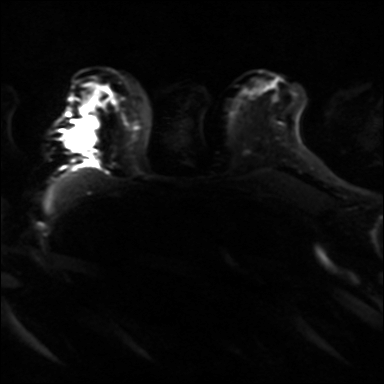
Breast MRI, one axial slice; position 24 of 36 along the scan axis; diffusion-weighted series; image 2 of 4 stored at this slice position (different b-values; order by instance number); 3 T; 4 mm slice thickness; 384 × 384 image matrix, field of view 320 × 320 mm. Female patient.
Structures marked on this image (manually delineated by an expert):
- tumour on diffusion-weighted imaging: bounding box [x1, y1, x2, y2] px = [63, 114, 99, 151]